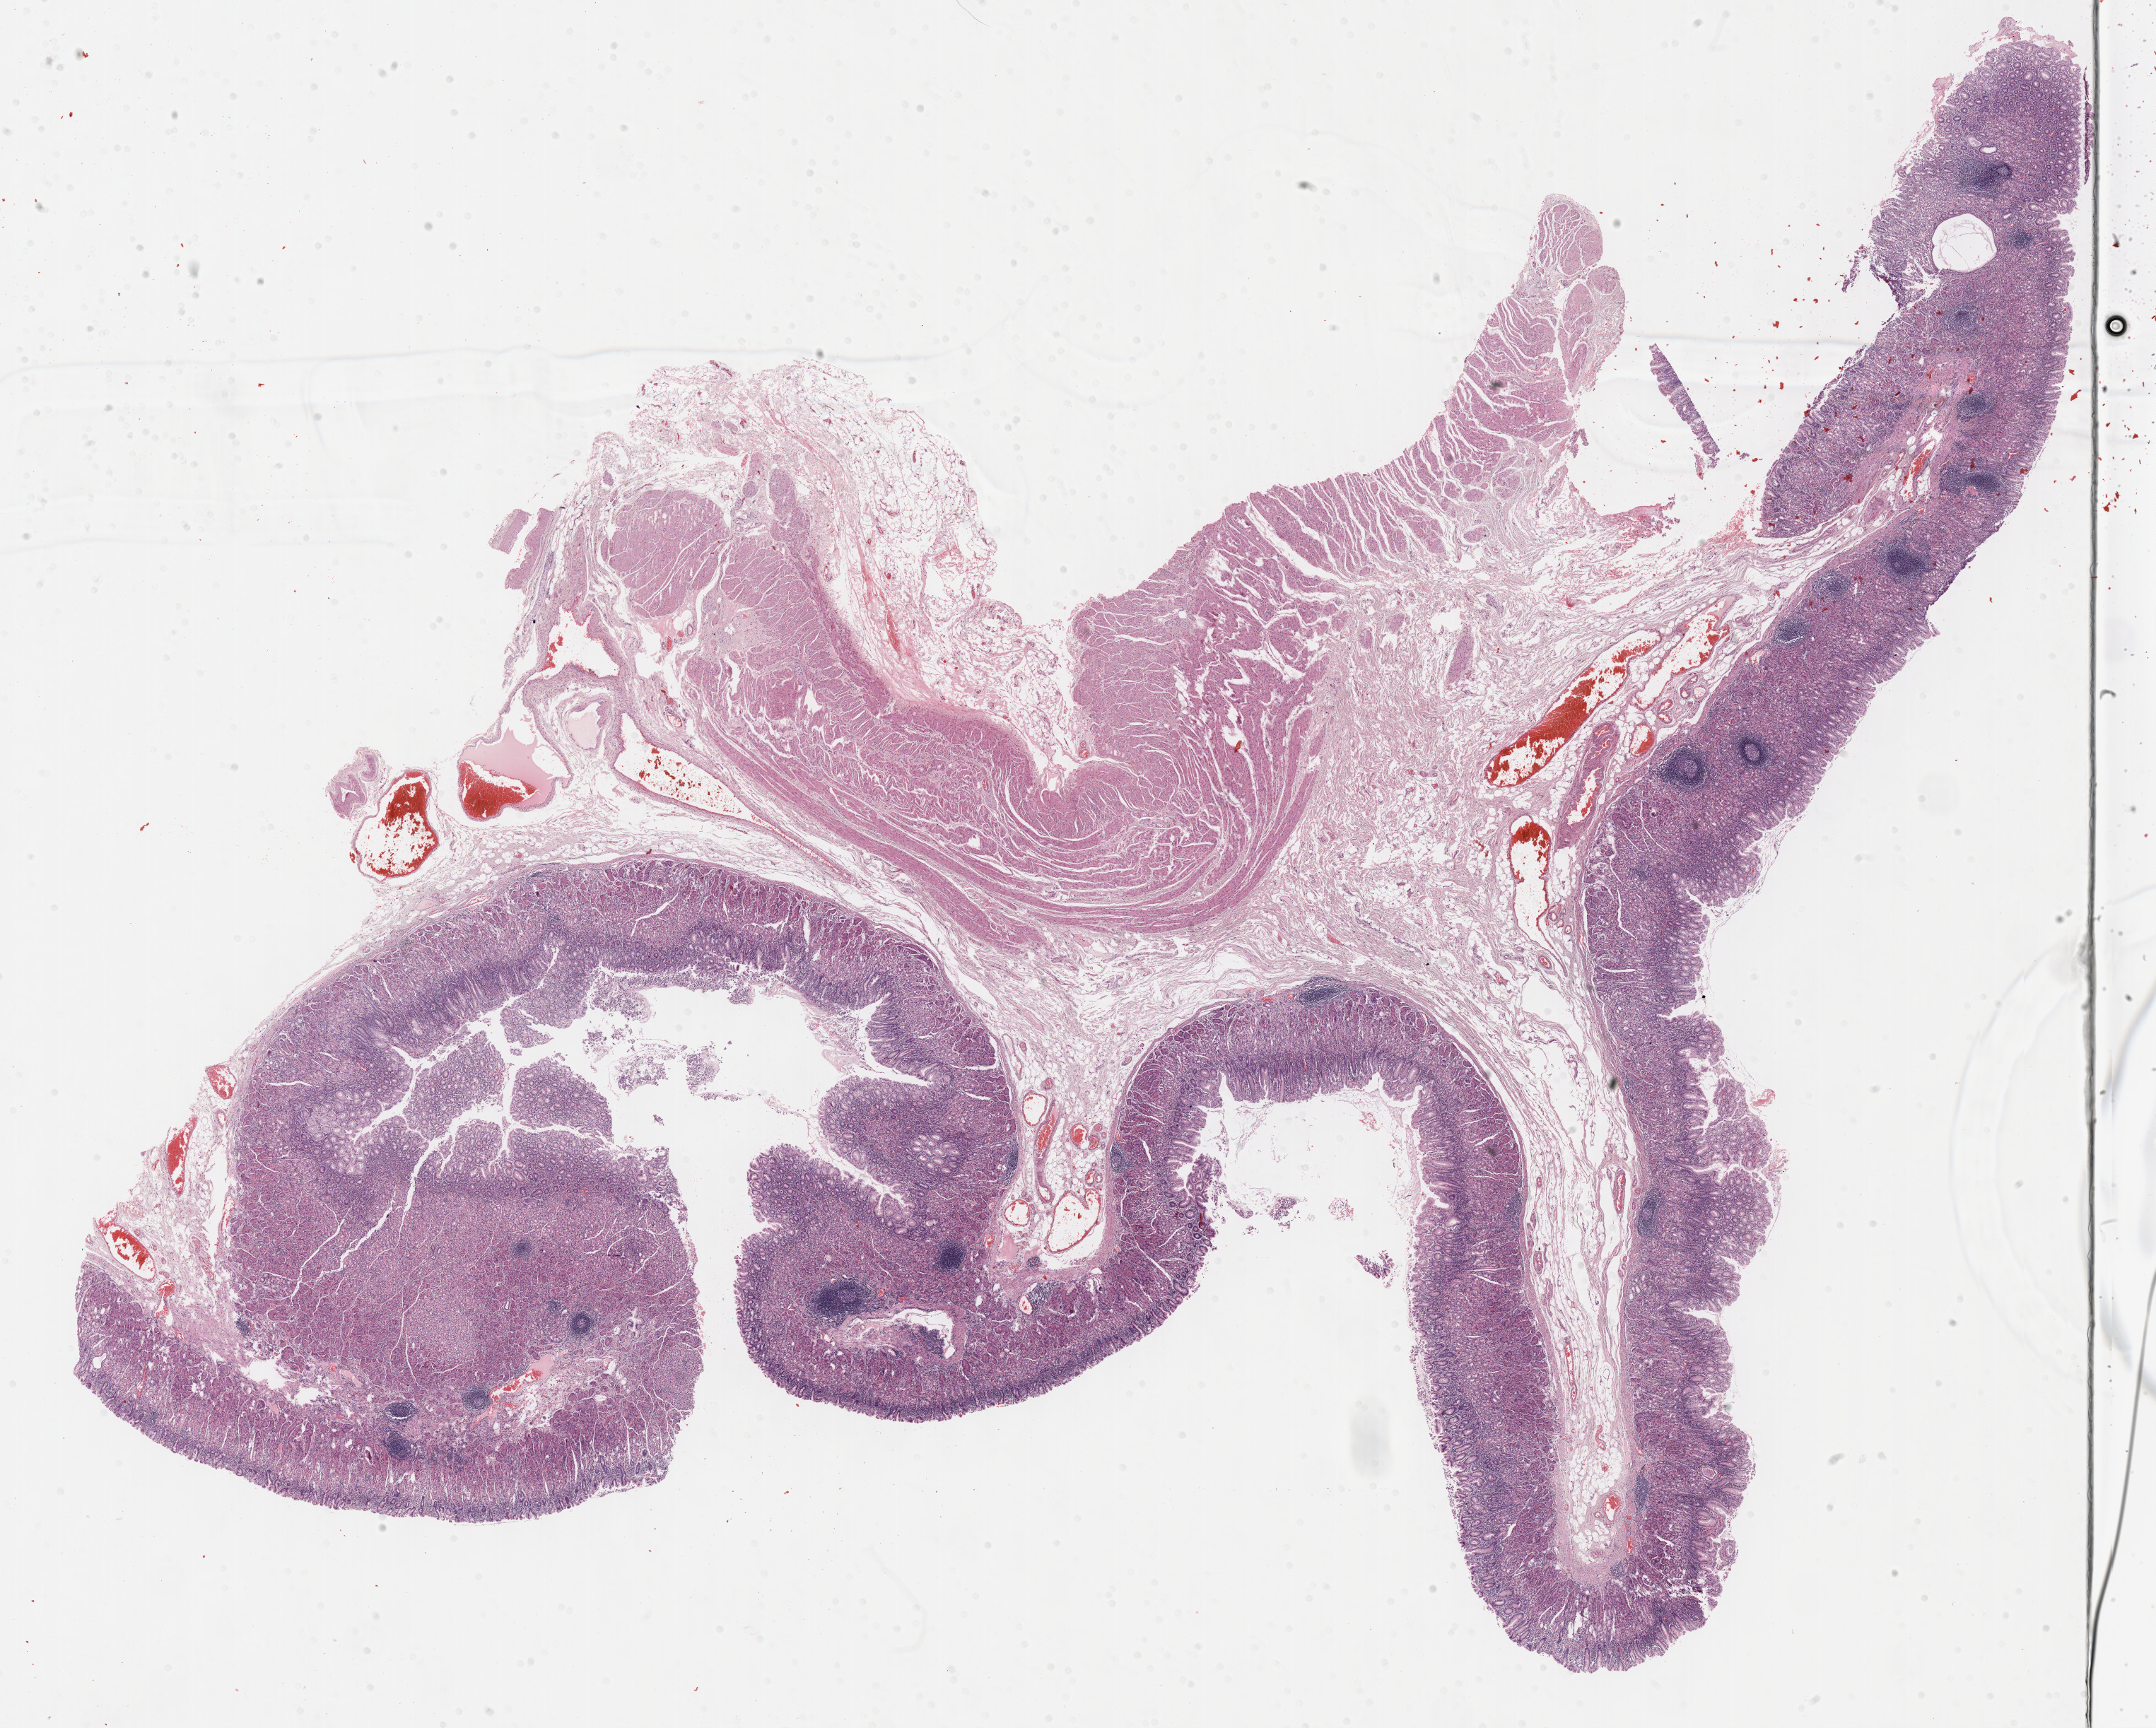
Digitized Hematoxylin and eosin (H&E) stained tissue section (whole slide) — whole scanned area (about 24.7 x 19.8 mm, acquisition: 40x scan) shown as a low-resolution overview. Formalin-fixed paraffin-embedded (FFPE) diagnostic section. Sample: primary tumour, stomach. Patient: male, age at initial diagnosis 57 years. Histologic grade: G3 (poorly differentiated).
Lymph nodes positive (case pathology): 0 of 8 examined. Diagnosis: Carcinoma, diffuse type. AJCC pathologic stage: IIB (7th edition).